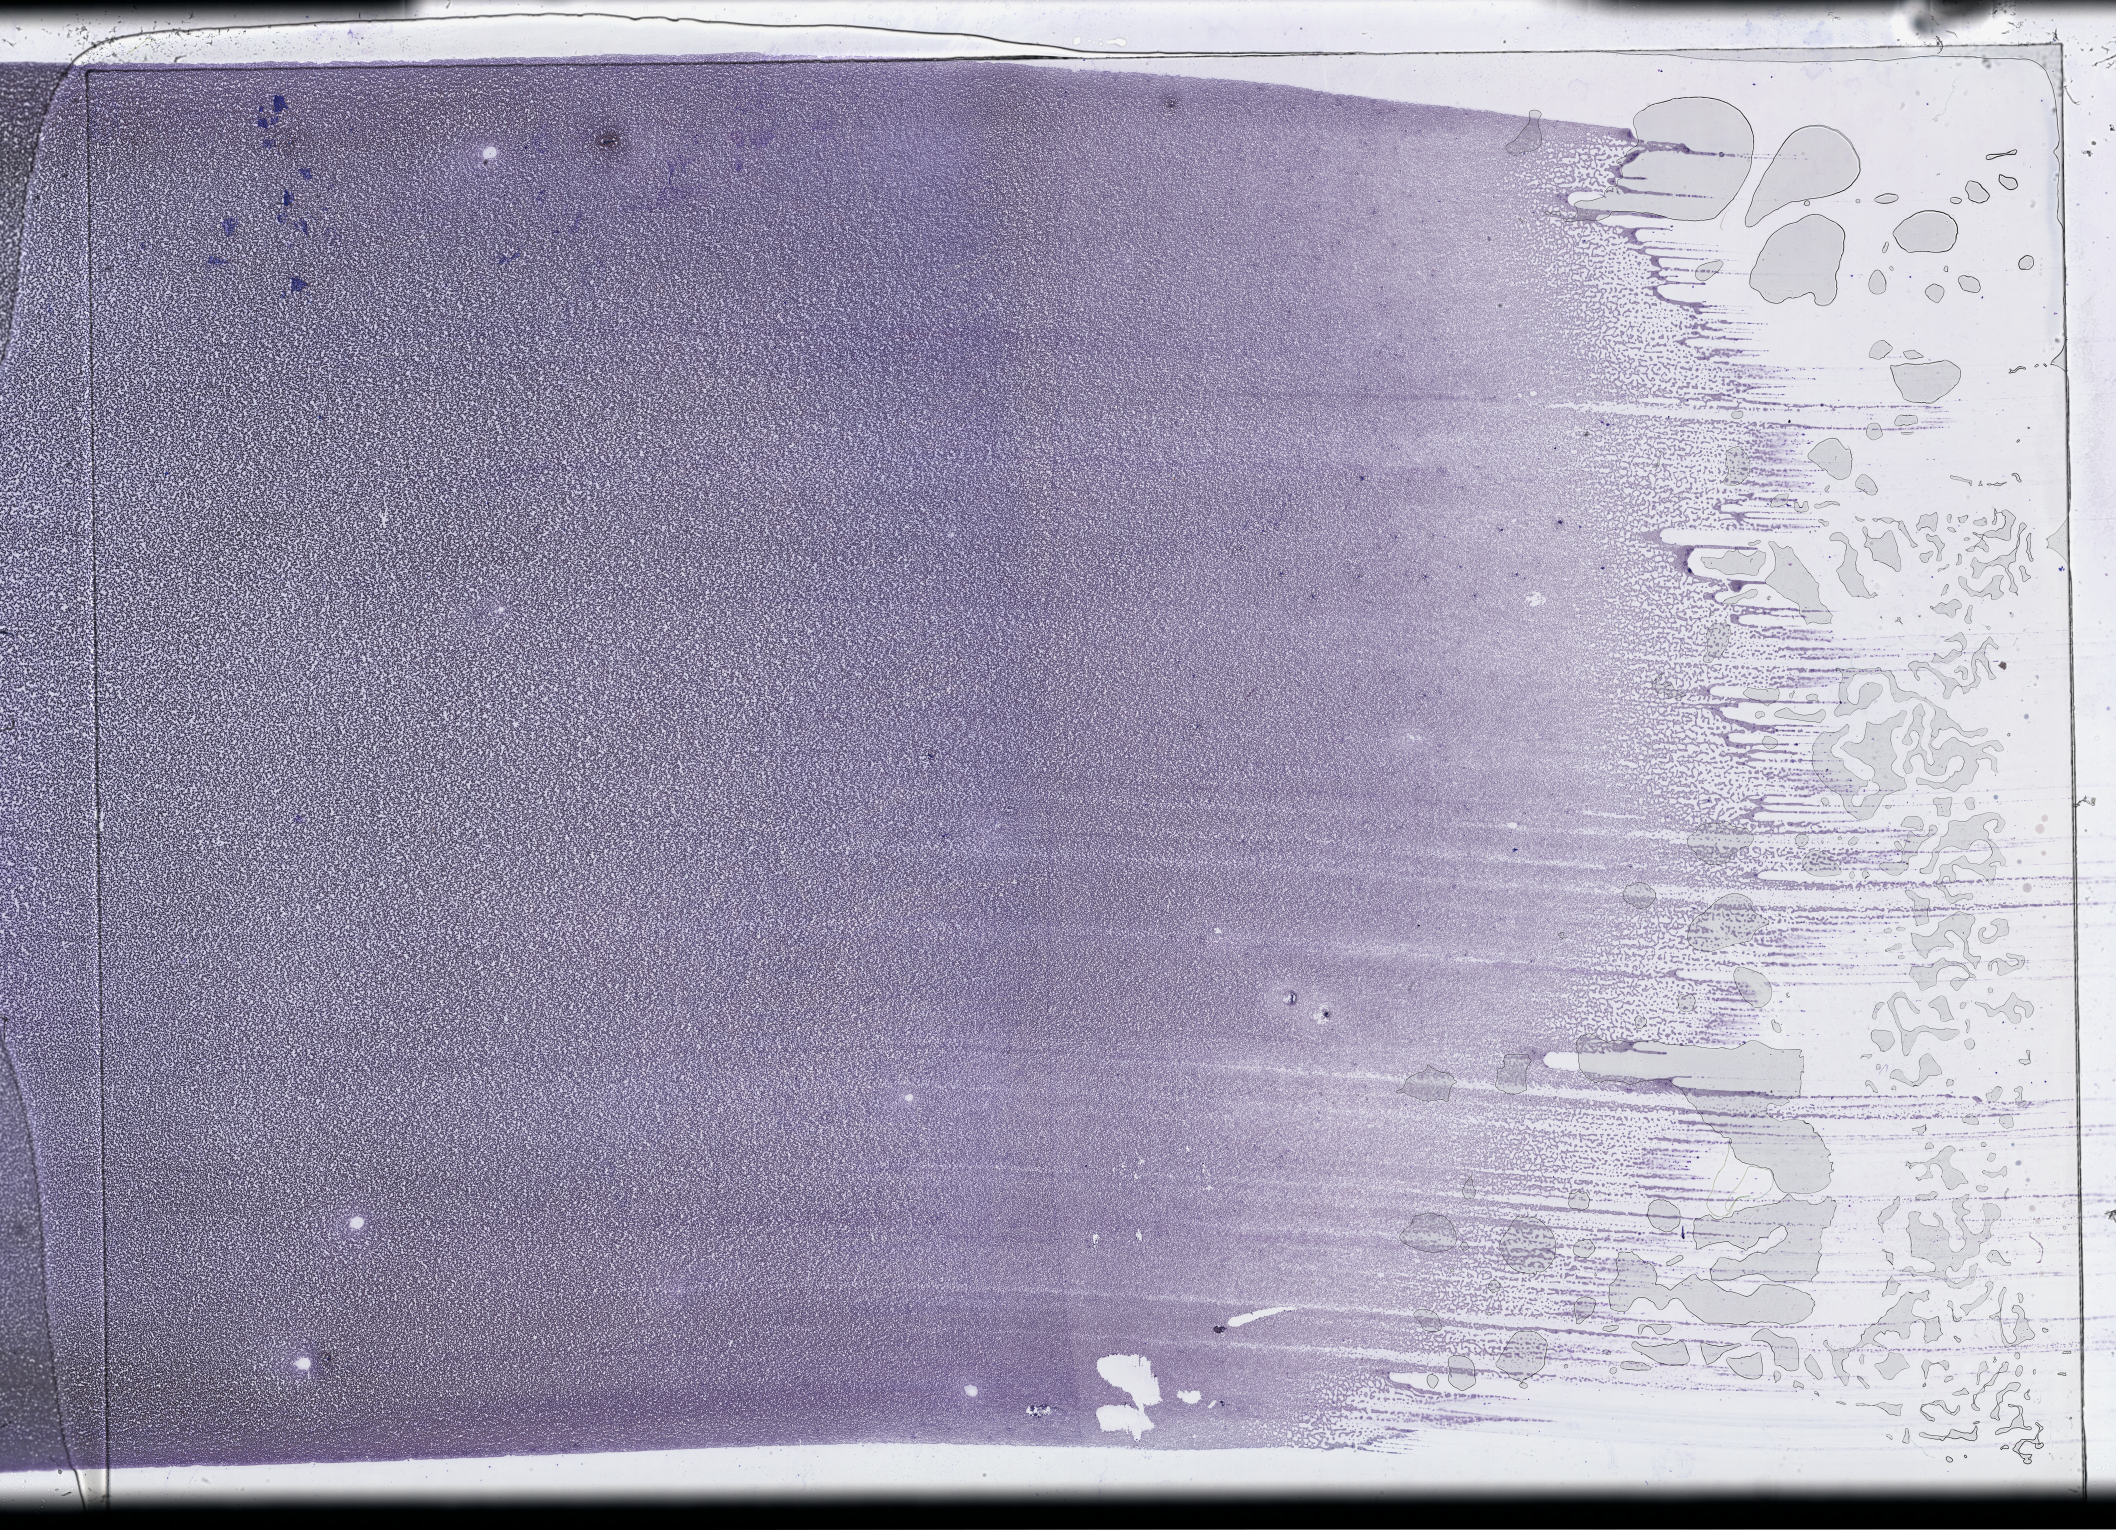
Digitized H&E-stained tissue section (whole slide), shown as a low-resolution overview of the whole scanned area (about 34.2 x 24.7 mm, slide scanned at 40x); peripheral blood (leukaemic) sample. Patient: male, age 70 years.
Diagnosis: Acute Myeloid Leukemia. FAB classification: M2.